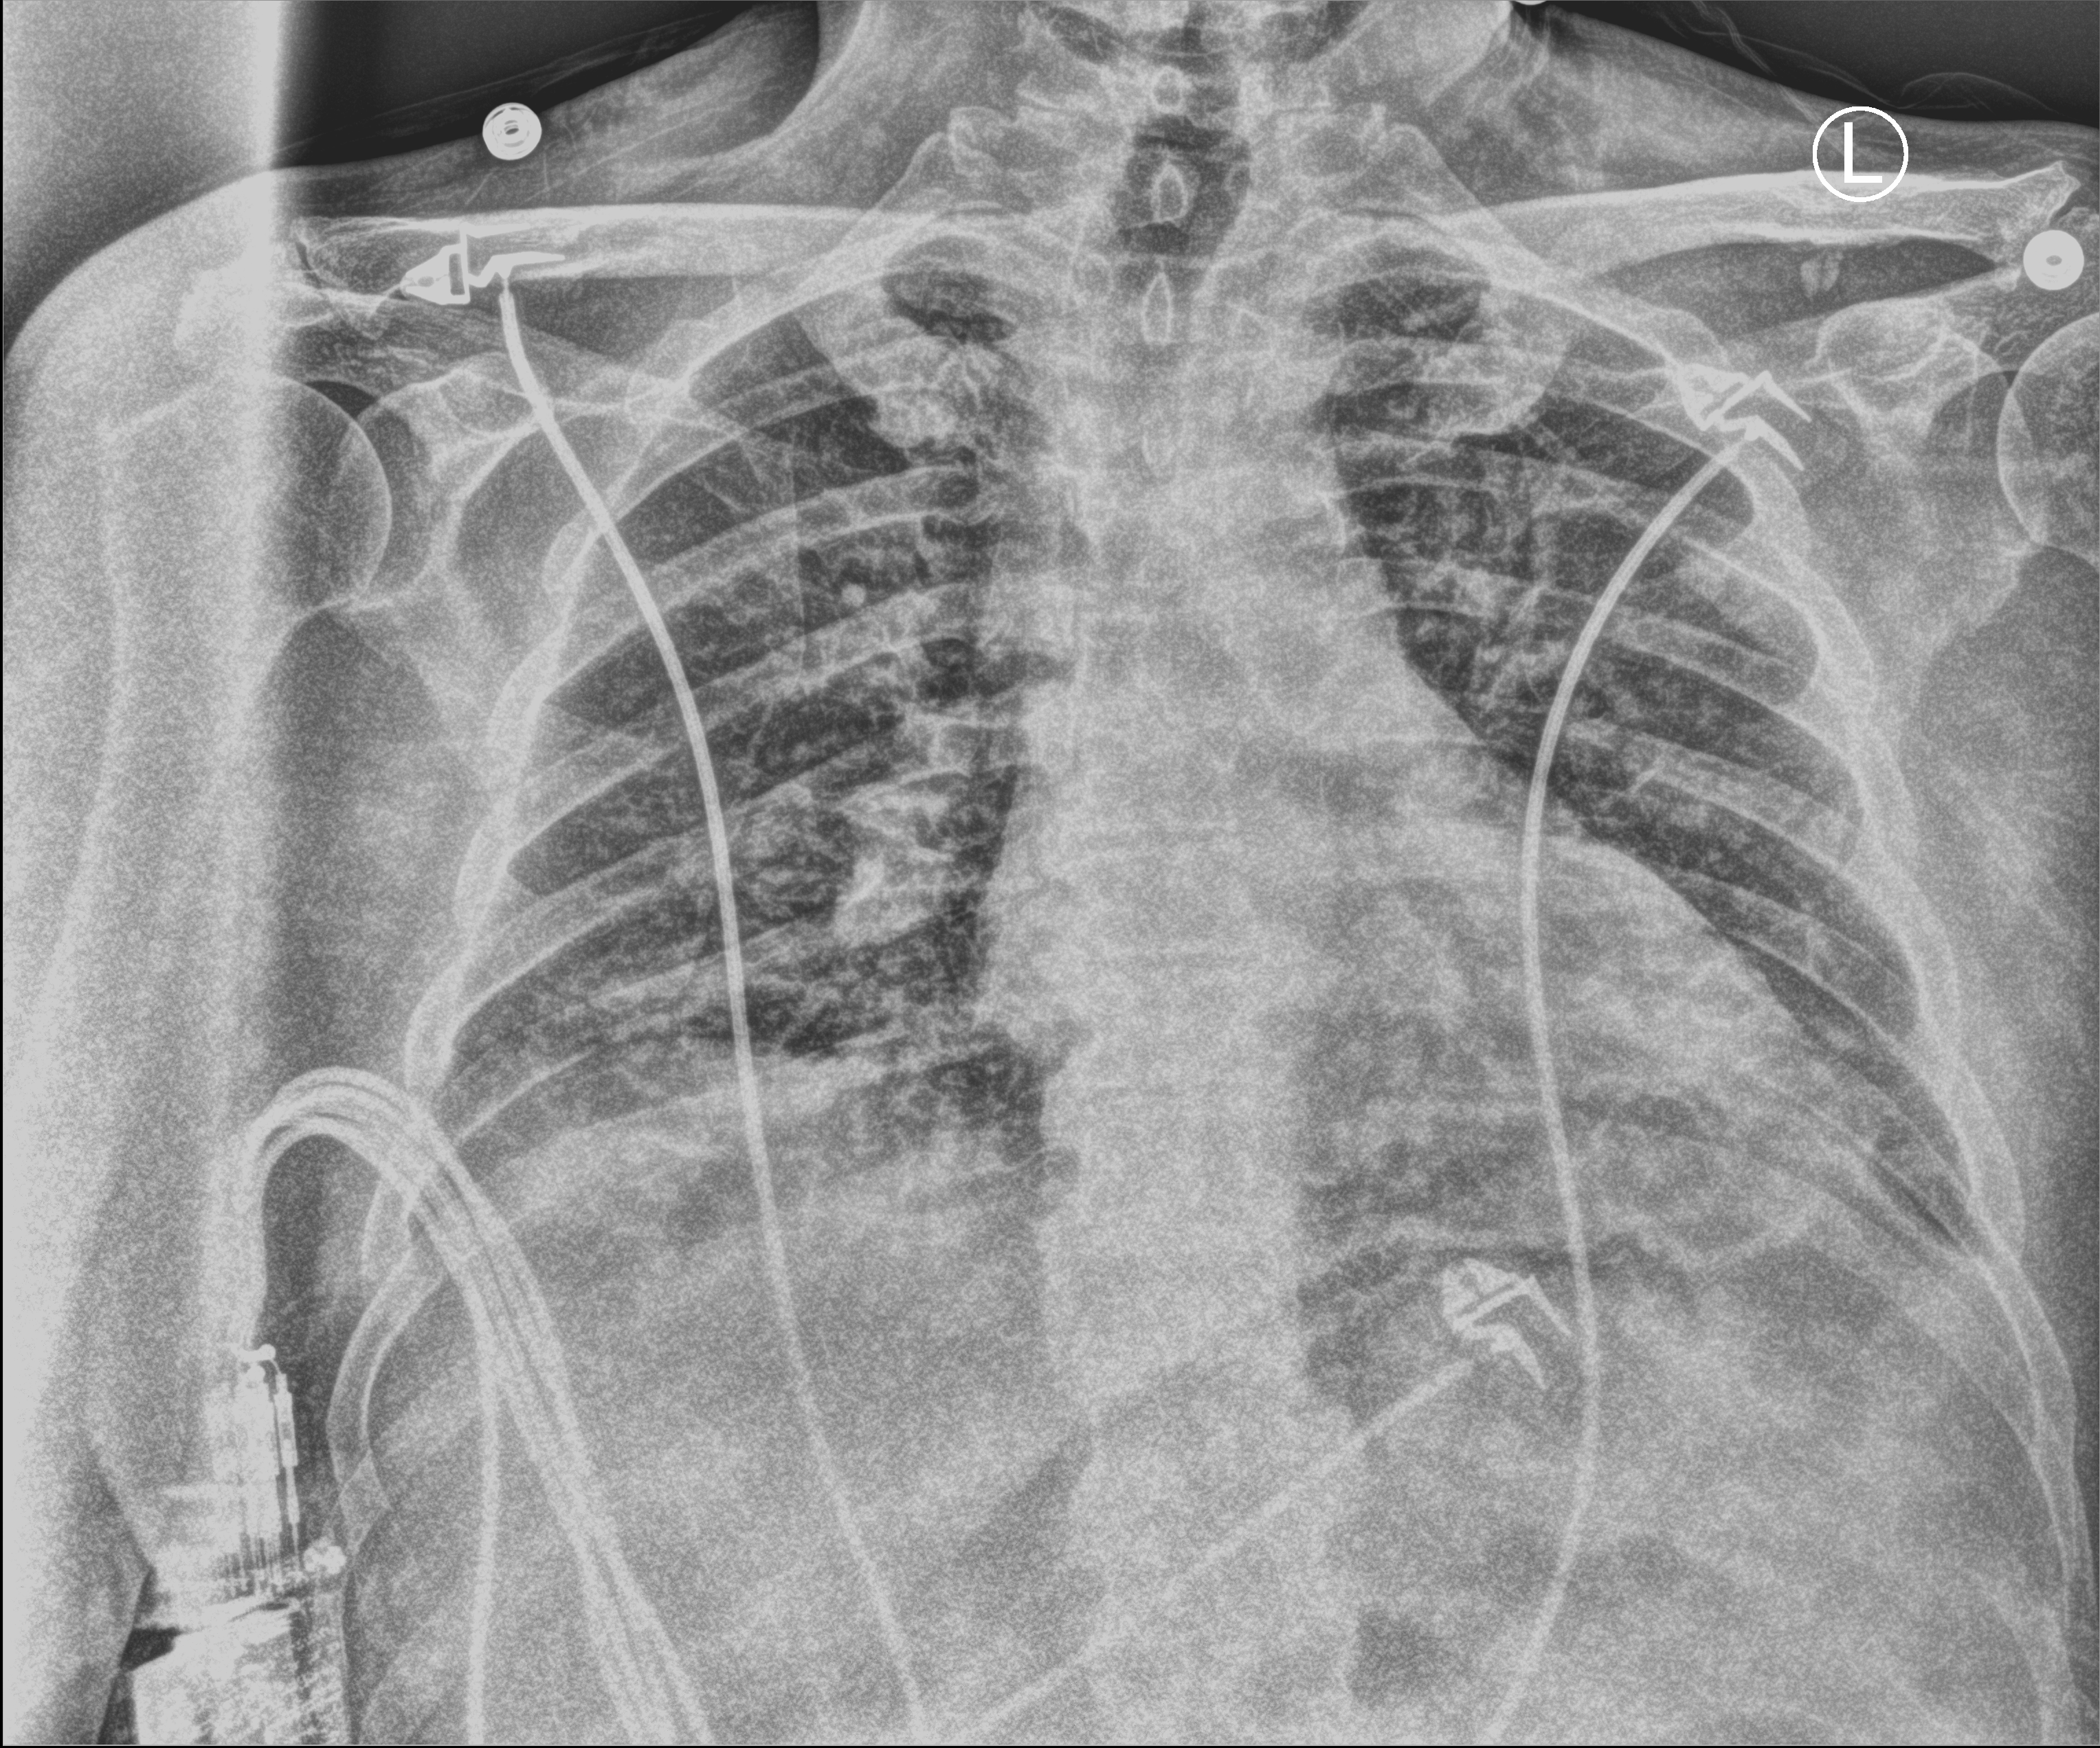
Portable chest radiograph; anteroposterior (AP) projection. Patient hospitalised with COVID-19; male, aged 18–59 years.
From the hospital-stay record, not from the radiograph (when in the stay this image was taken is not recorded):
- admitted to intensive care during this hospital stay: no
- mechanically ventilated during this hospital stay: no
- length of hospital stay: 13 days